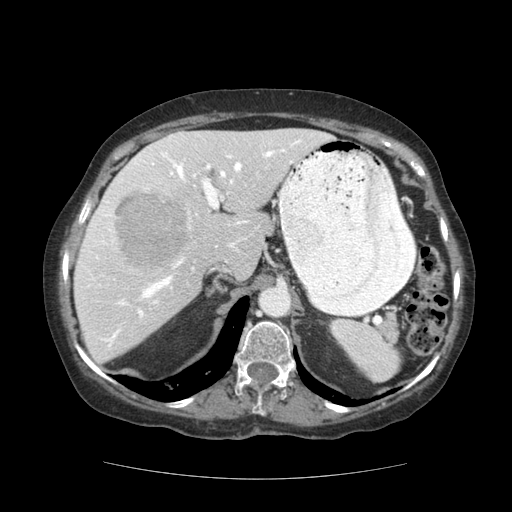
Contrast-enhanced abdominal CT (liver protocol), one axial slice; position 80 of 111 along the scan axis; reconstruction kernel STANDARD; 140 kVp; soft-tissue window (W 400 / L 40 HU); 2.5 mm slice thickness; 512 × 512 image matrix, field of view 360 × 360 mm. Case-level facts recorded for this patient, not image findings: diagnosis: hepatocellular carcinoma (patient treated with transarterial chemoembolisation; whether this scan precedes or follows treatment is not stated here); TNM stage (as recorded): Stage-I.
Annotated regions visible in this slice (semi-automatic segmentation, software-assisted and operator-edited):
- liver parenchyma outside the tumour (the mass and vessels are separate outlines, so this box may not span the whole liver): bounding box <74,128,332,362> (left, top, right, bottom; pixels)
- mass: <115,189,188,267>
- liver vessels: <83,136,301,347>